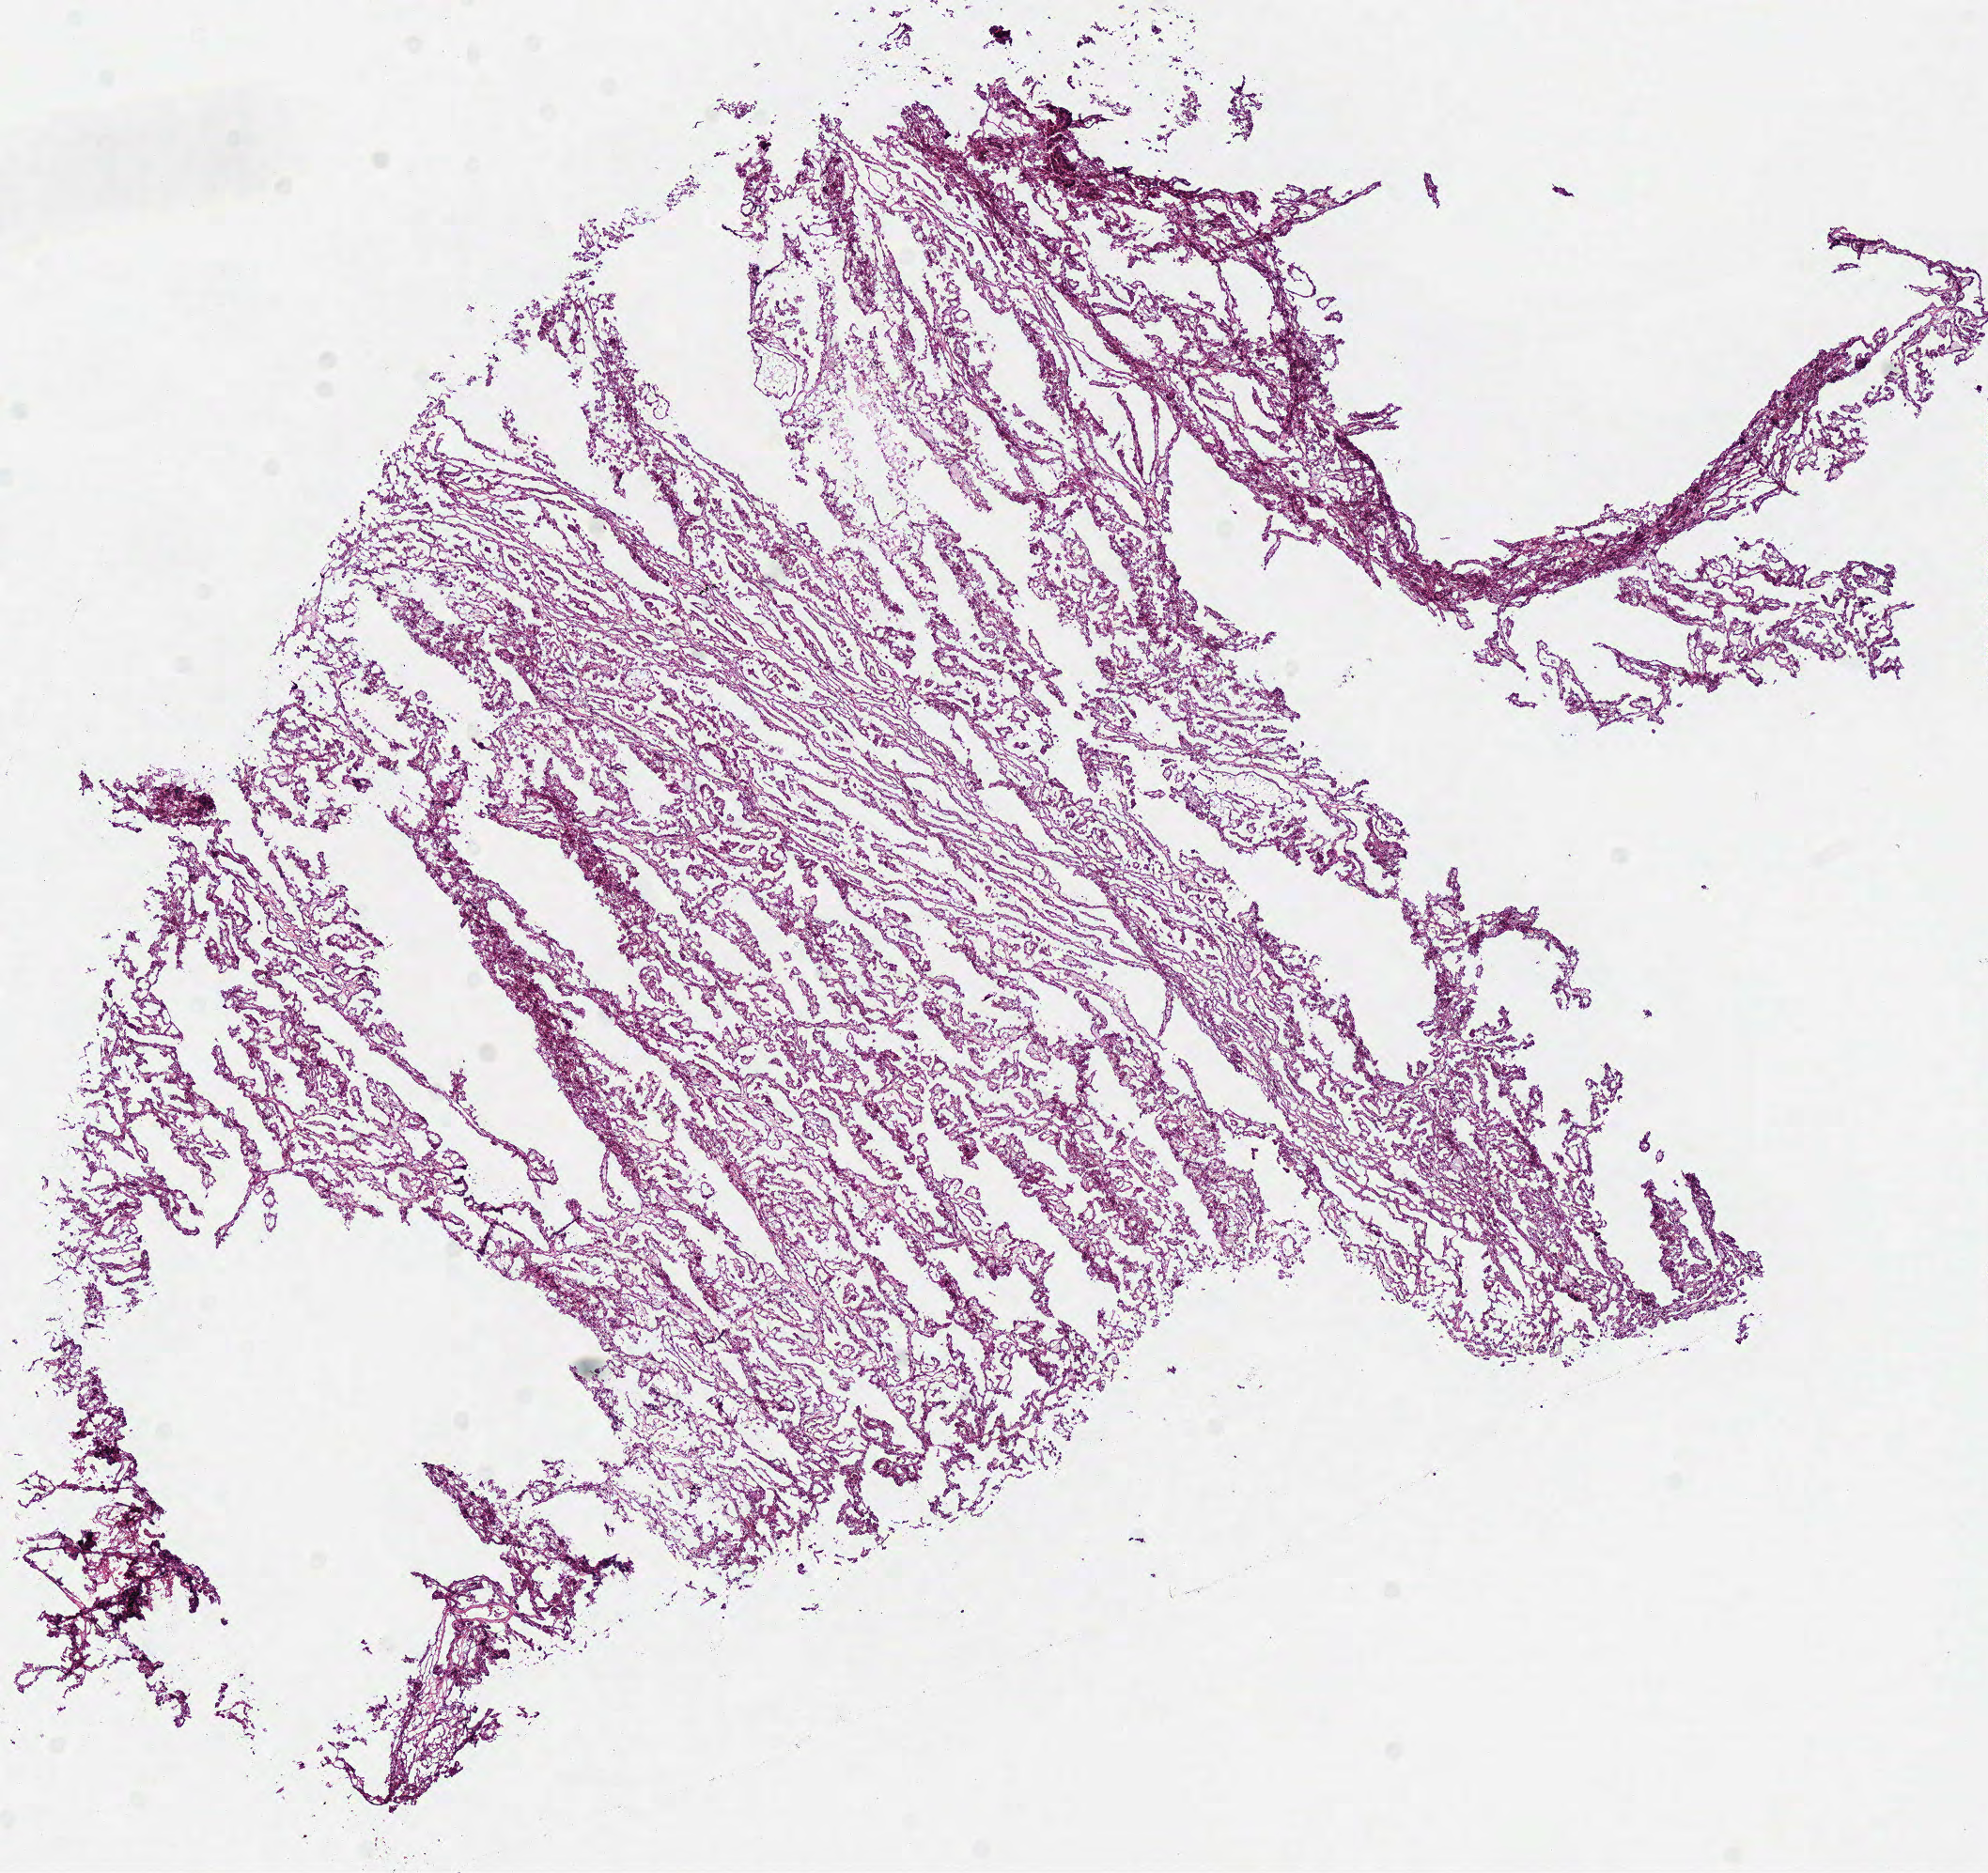
Digitized H&E-stained tissue section (whole slide), low-resolution overview of the scanned area, about 8.3 x 7.8 mm (acquisition: 40x scan), frozen section from the bottom of the tissue portion, sample: primary tumour, kidney. Patient: male, age at initial diagnosis 56 years. Slide review estimates, as recorded: tumour cells 100%, tumour nuclei 85%, normal cells 0%, stromal cells 0%, necrosis 0%.
Pathologic diagnosis: Papillary adenocarcinoma, NOS. AJCC pathologic stage: I.